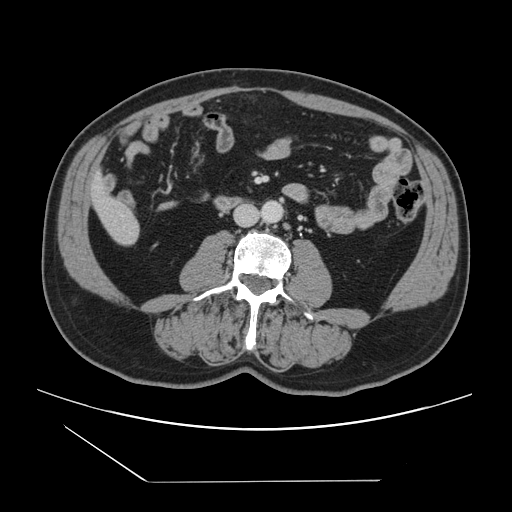
Contrast-enhanced abdominal CT, one axial slice; position 18 of 157 along the scan axis; 120 kVp; intravenous contrast given; soft-tissue window (W 400 / L 40 HU); 2.5 mm slice thickness; 512 × 512 image matrix. Male patient, age 61 years. From the clinical record (not read from this slice): diagnosis: colorectal cancer liver metastases, imaged before liver resection; multiple liver metastases: yes; largest metastasis: 5.5 cm; chemotherapy before resection: no.
Structures marked on this image (outlined manually by an expert reader):
- liver: bounding box [x1, y1, x2, y2] px = [92, 177, 140, 245]
- planned liver remnant (the part of the liver to remain after resection): [93, 177, 124, 217]